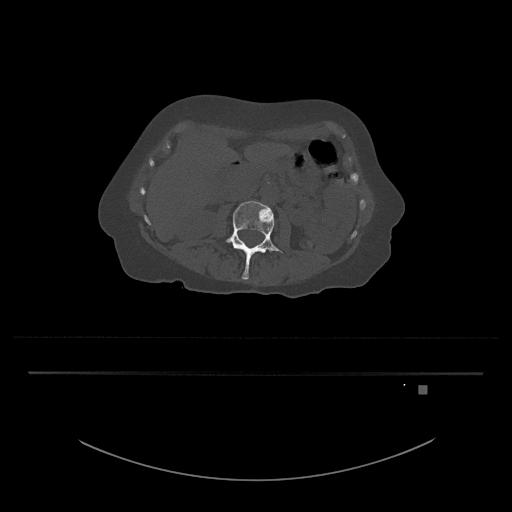
CT including the spine, one axial slice. Position 429 of 797 along the scan axis. Reconstruction kernel Br40s/3. Bone window (W 1800 / L 400 HU). 0.5 mm slice thickness. 512 × 512 image matrix, field of view 500 × 500 mm. Patient: female, 57 years. From the clinical record (not read from this slice): primary cancer: cervical.
Annotated regions visible in this slice (semi-automatic segmentation, software-assisted and operator-edited):
- L3 vertebra: box from (x=225, y=201) to (x=283, y=280) px